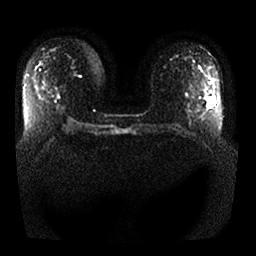
Breast MRI, one axial slice; position 15 of 25 along the scan axis; diffusion-weighted series; image 2 of 4 stored at this slice position (different b-values; order by instance number); 1.5 T; 256 × 256 image matrix, field of view 360 × 360 mm. Female patient.
Structures marked on this image (manually delineated by an expert):
- tumour on diffusion-weighted imaging: bounding box <208,97,215,108> (left, top, right, bottom; pixels)